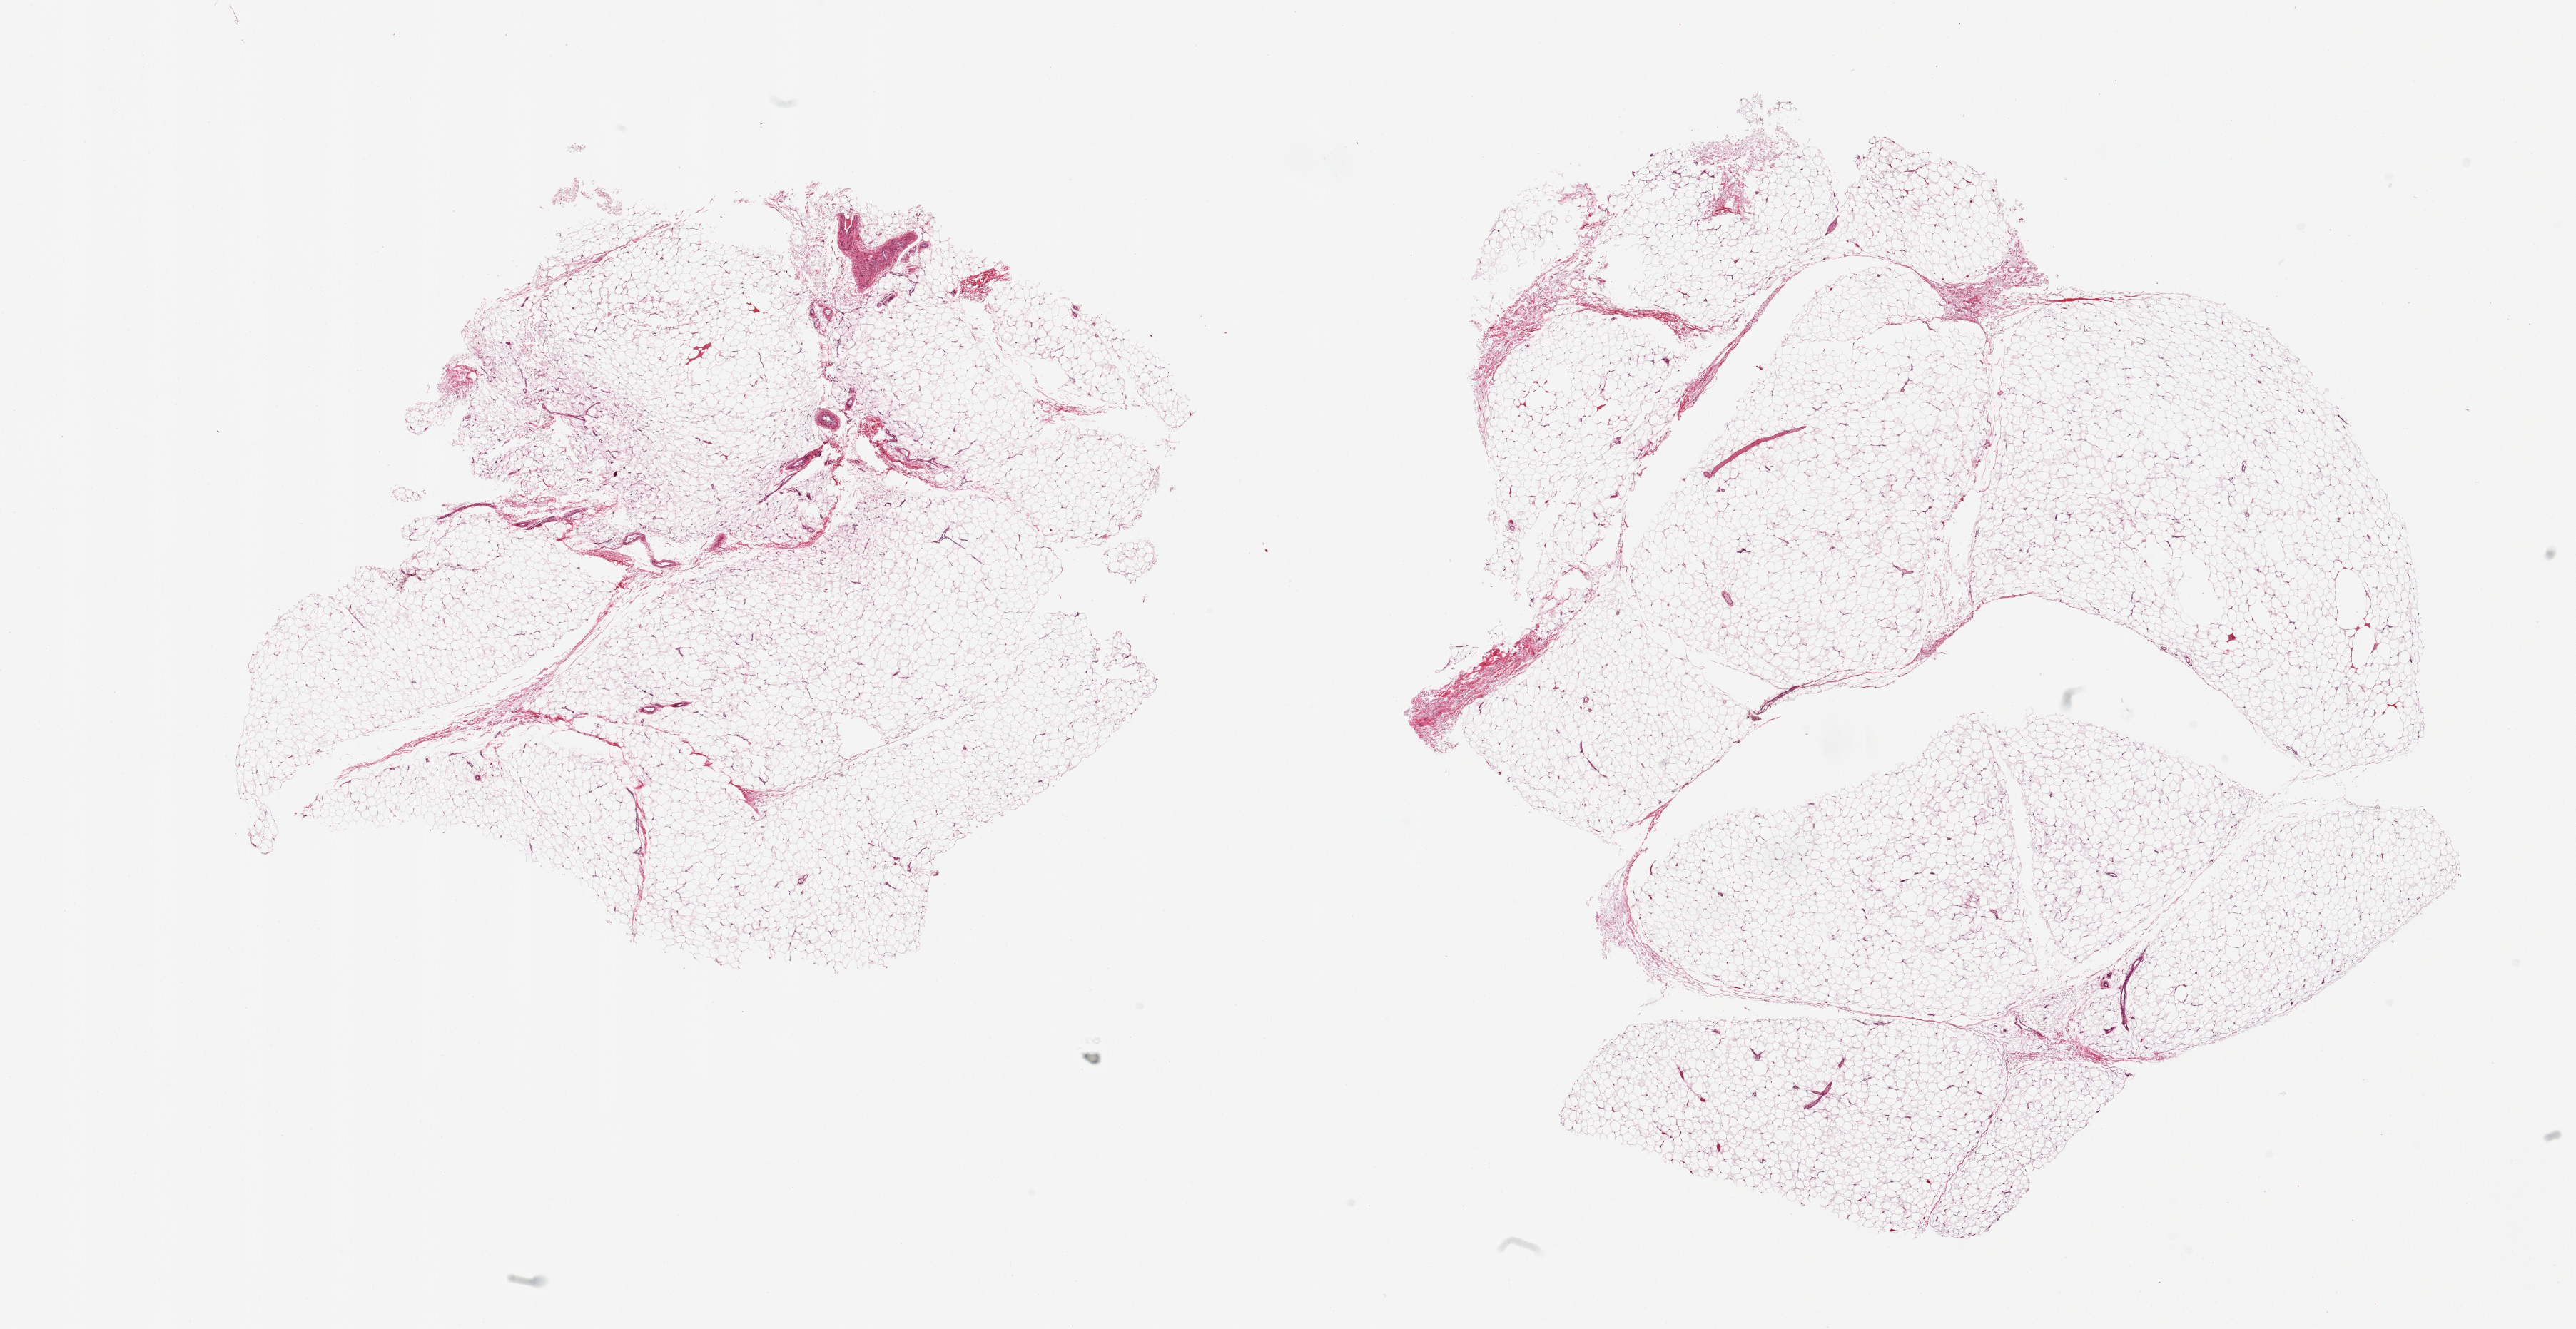
Digitized H&E-stained section, brightfield, shown as a low-resolution overview of the whole scanned area (about 28.5 x 14.7 mm, acquisition: 20x scan), PAXgene-fixed, paraffin-embedded tissue, target tissue: adipose tissue, tissue donor sample. Female donor.
Pathologist's review note for this sample: 2 pieces.